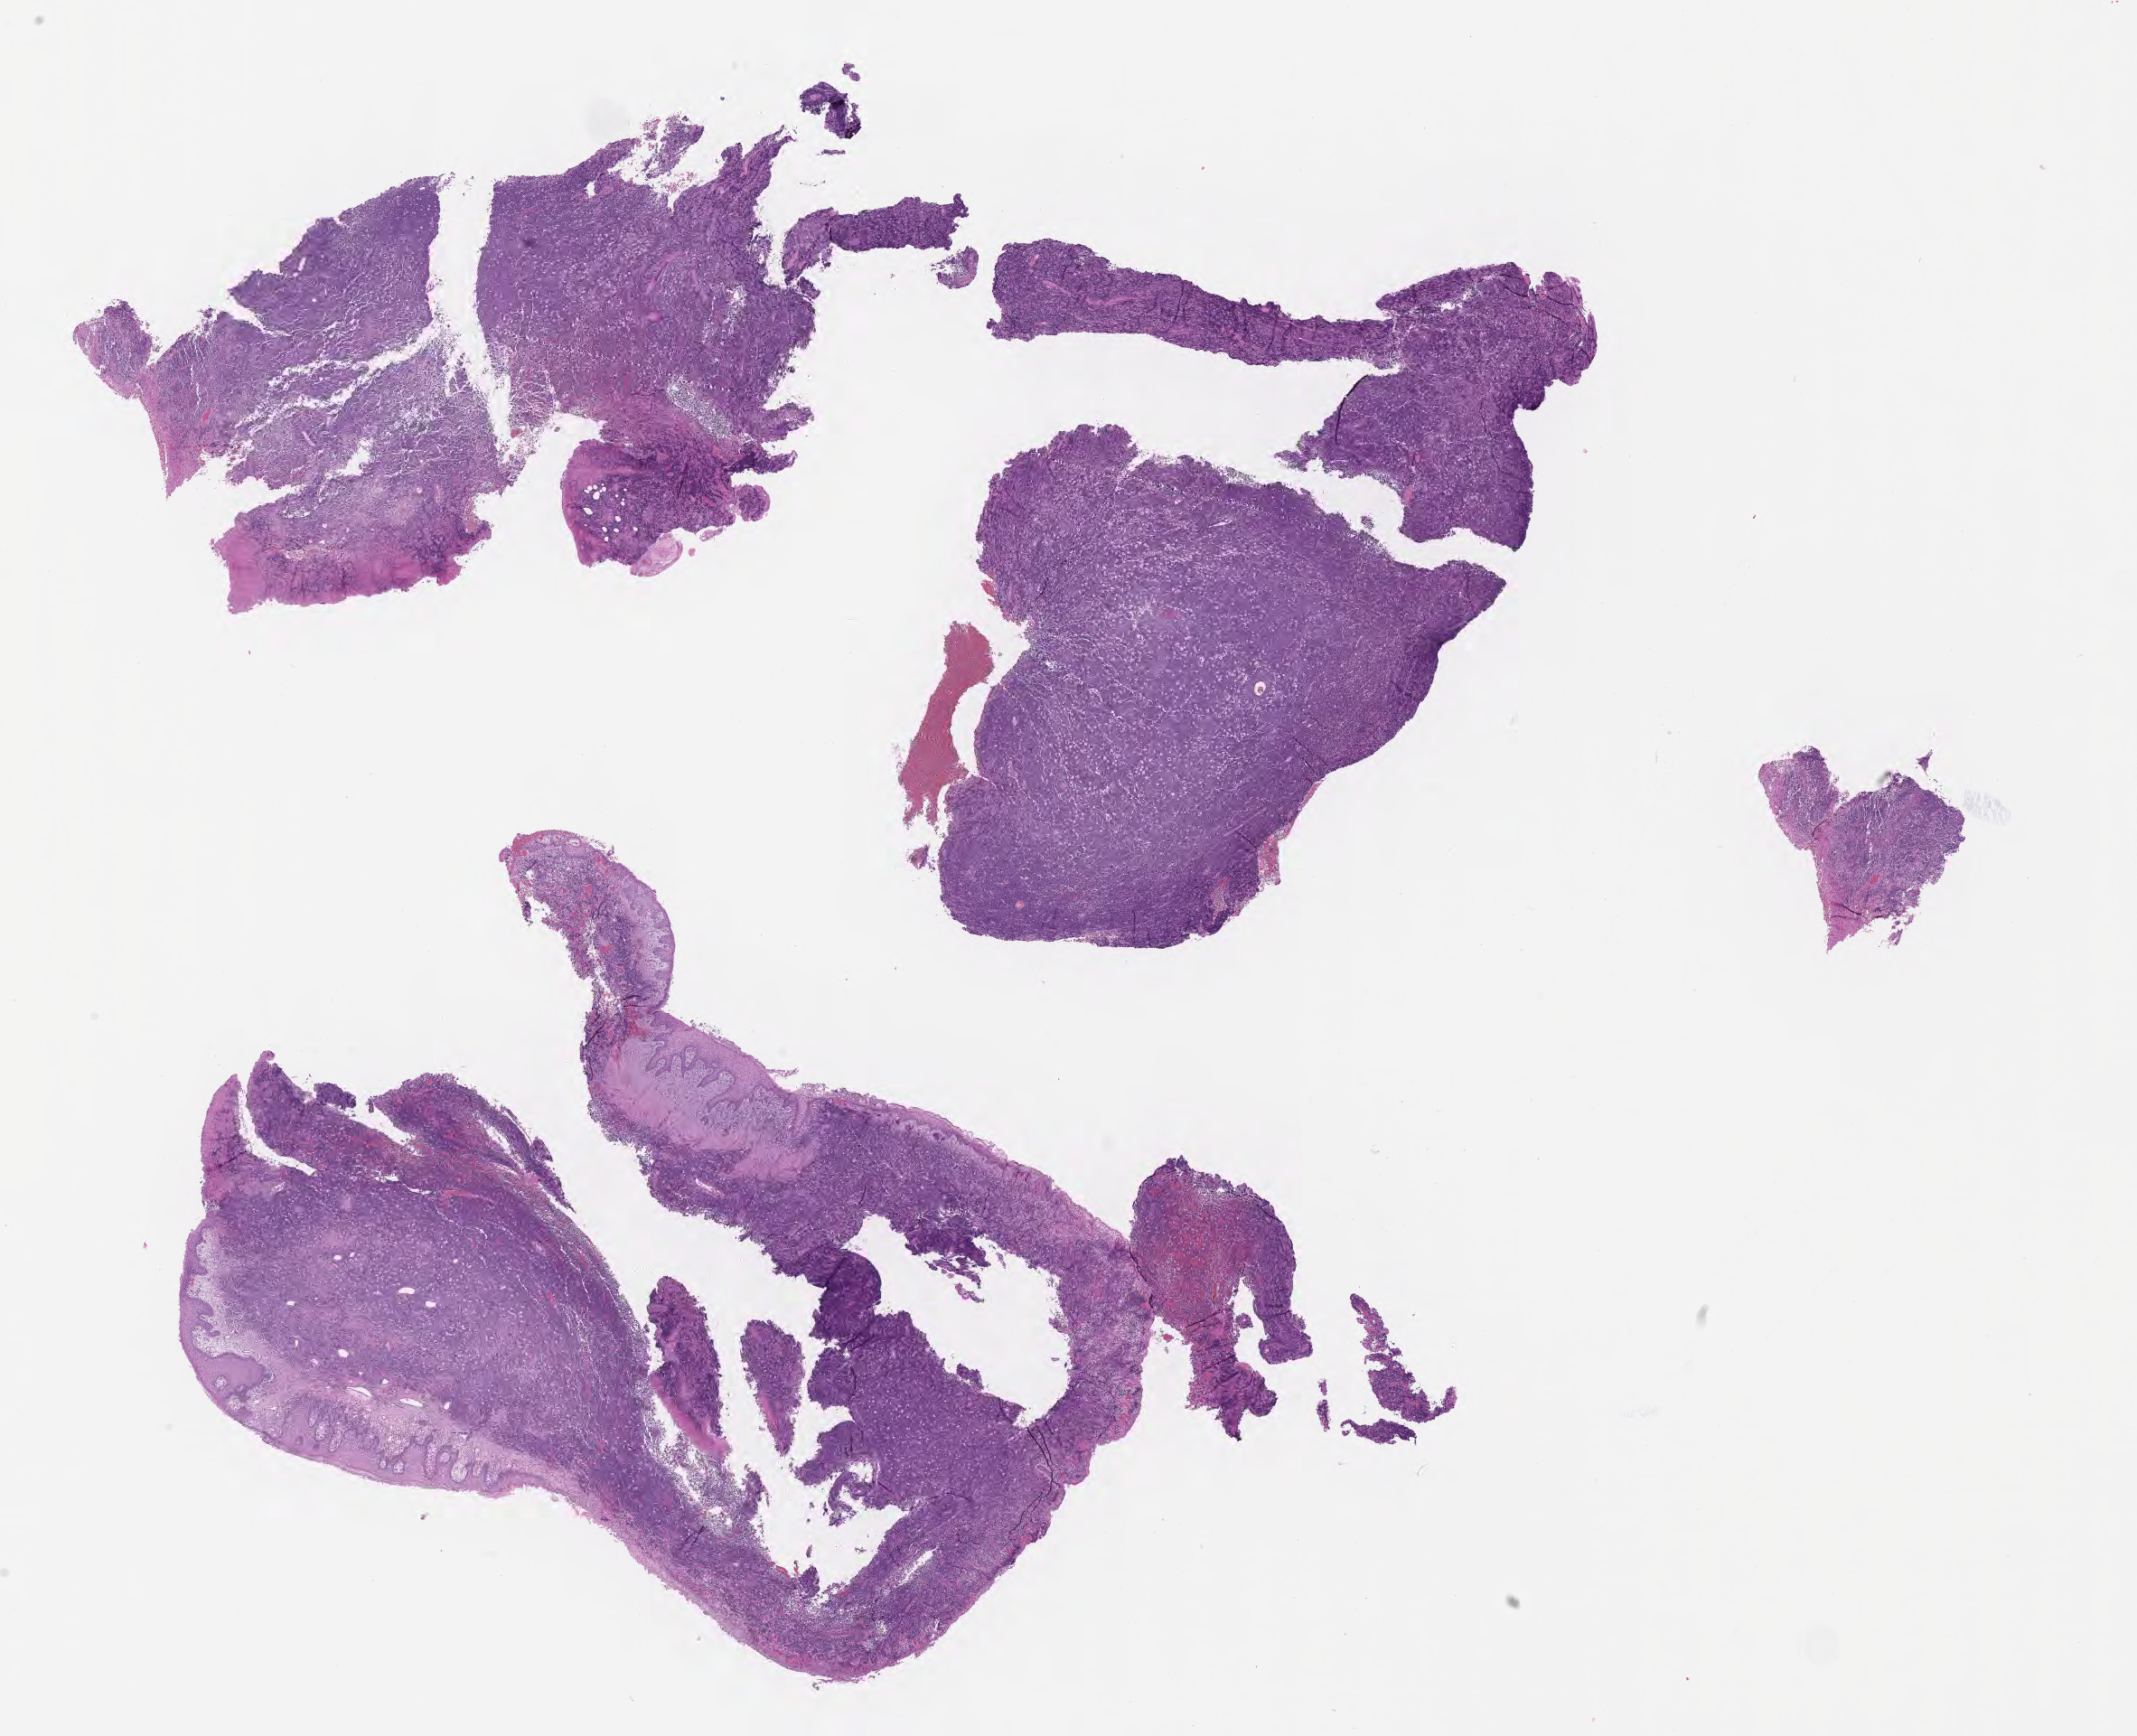
Whole-slide image, hematoxylin and eosin (H&E) stain, a low-resolution overview of the entire scanned area, about 19.1 x 15.5 mm. Formalin-fixed paraffin-embedded section. Specimen: primary tumor. Male patient, 22 years old. Pathologist review of this section (percent, as recorded): tumor cells 80%, tumor nuclei 90%, stromal cells 5%, necrosis 5%, normal cells 10%. Infiltration values recorded for this section: lymphocyte infiltration 80%, monocyte infiltration 10%, neutrophil infiltration 0%.
• histologic diagnosis: Burkitt lymphoma, NOS
• Ann Arbor stage (patient): Stage IV